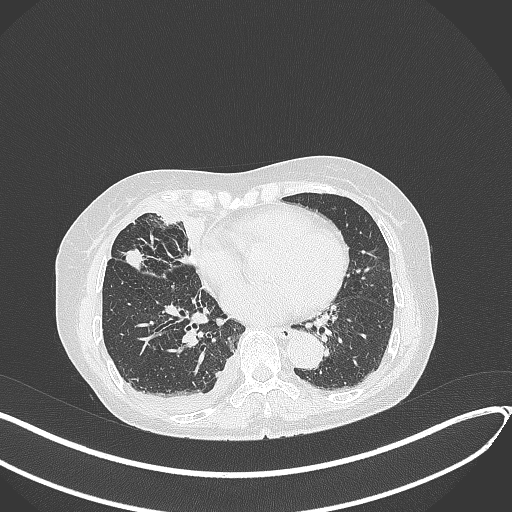
Chest CT, one axial slice. Position 158 of 418 along the scan axis. 120 kVp. Lung window (W 1500 / L -600 HU). 1 mm slice thickness. 512 × 512 image matrix. Female patient, age 75 years. Case-level facts recorded for this patient, not image findings: clinical TNM (as recorded): T2a N3 M0.
Annotated regions visible in this slice (rectangle marked by the reading radiologist):
- lung tumour (recorded histology: adenocarcinoma): box from (x=123, y=247) to (x=147, y=274) px